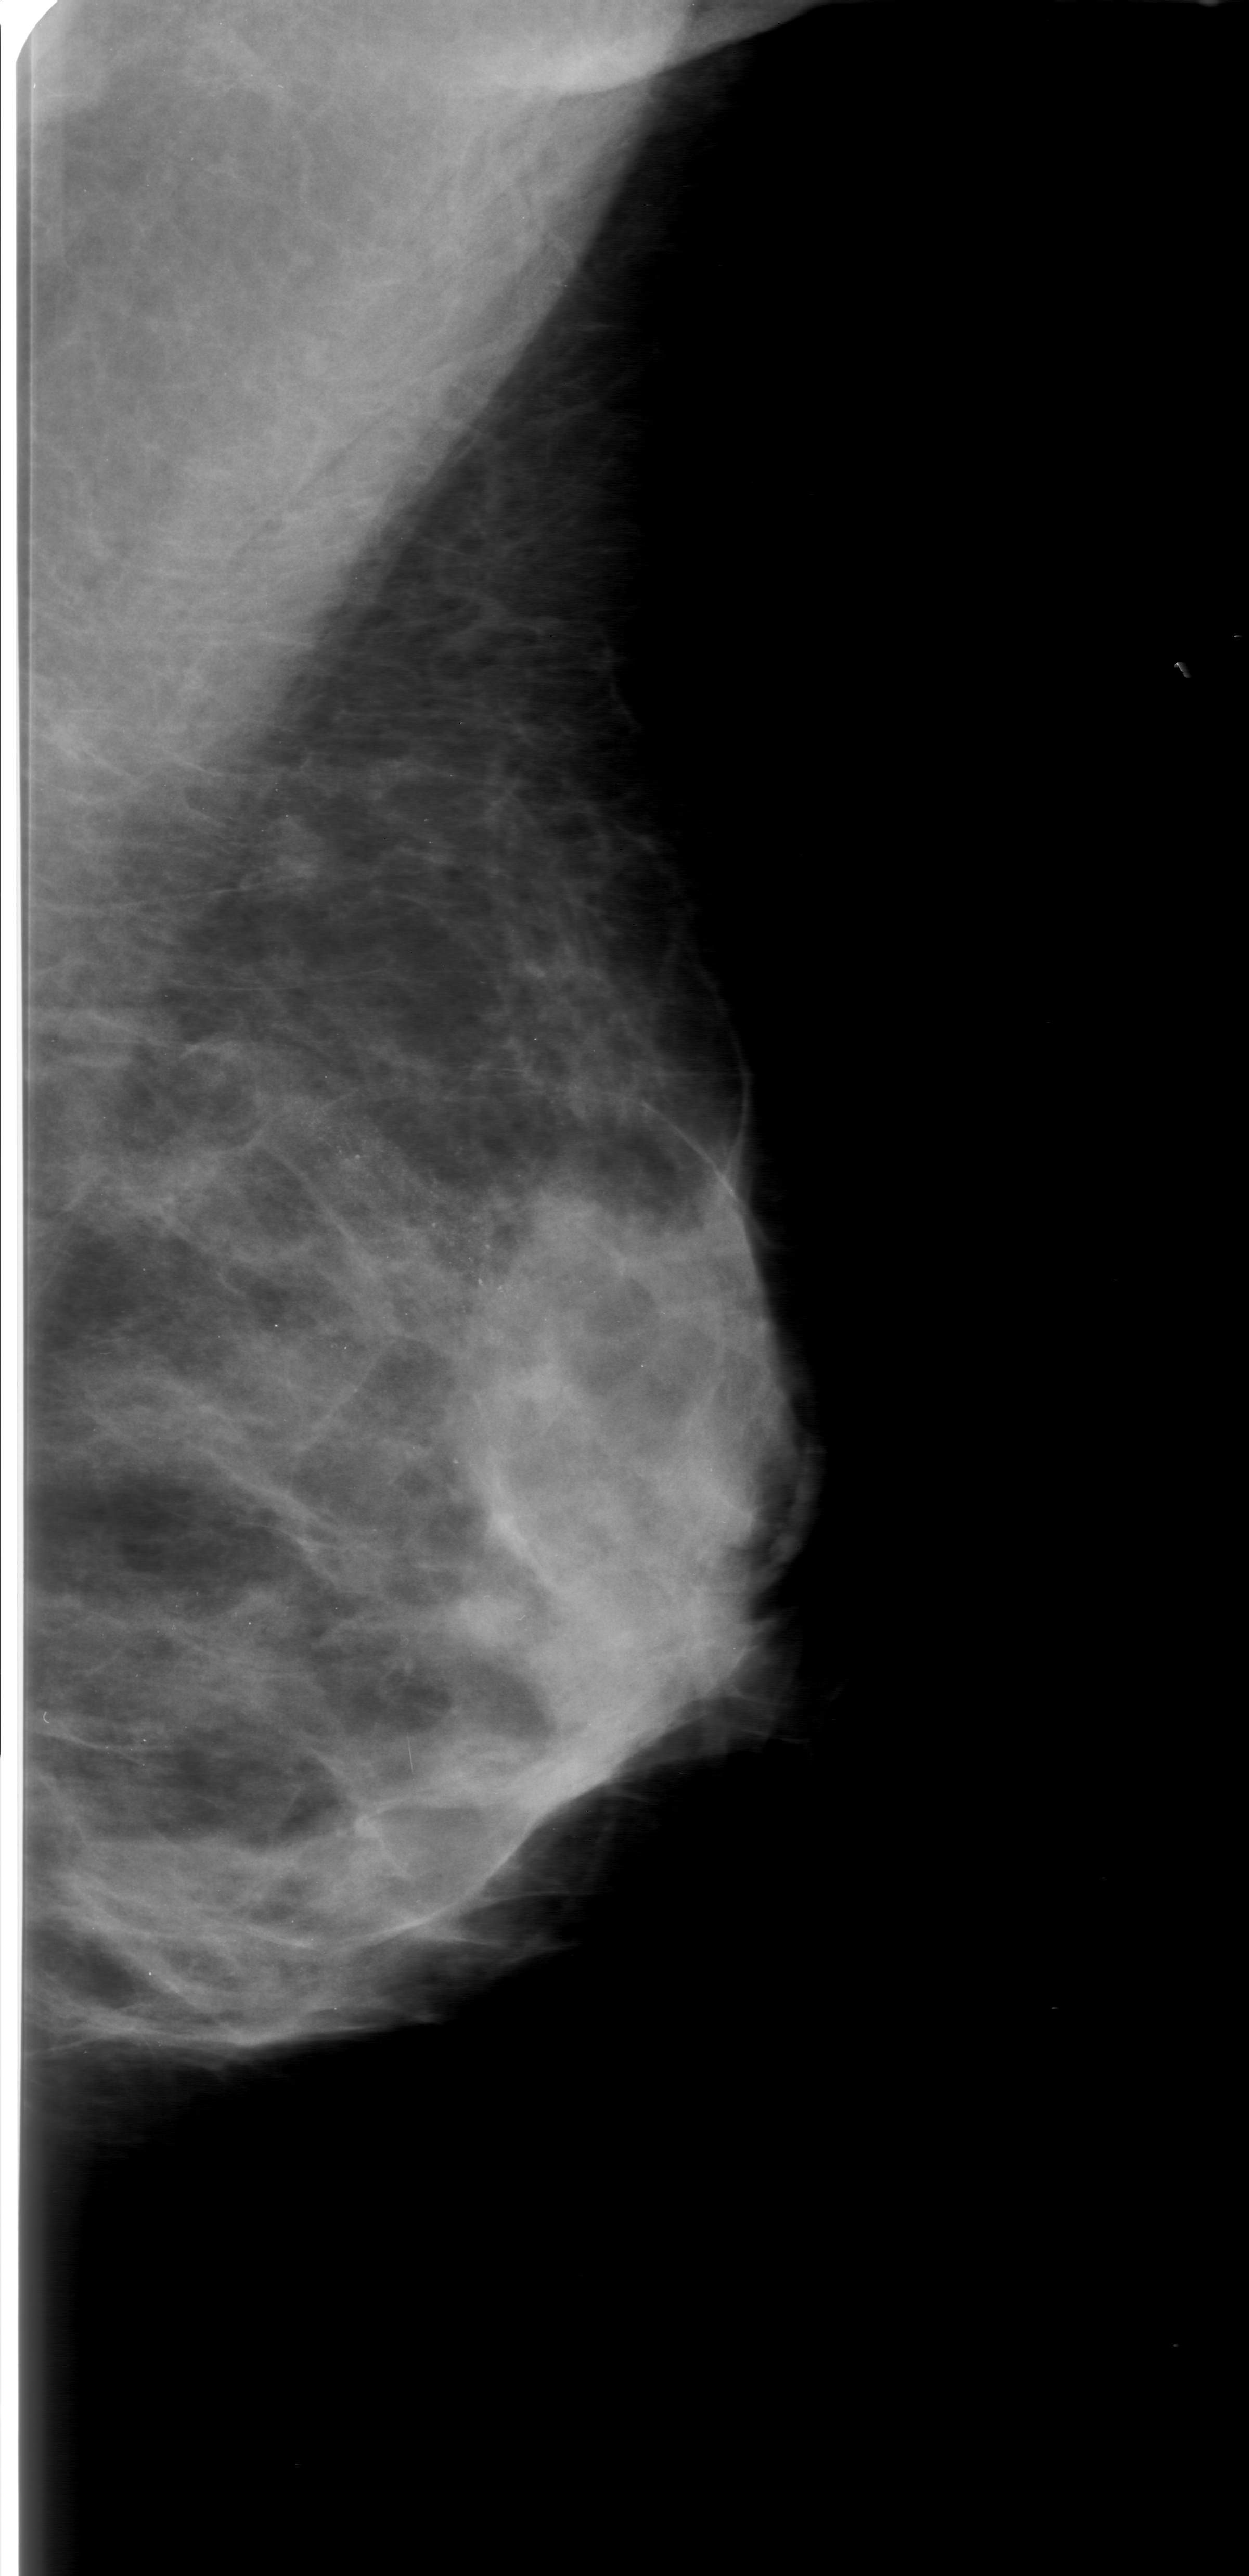
Mammogram (digitized film); left breast; mediolateral oblique (MLO) view; BI-RADS breast density category 3 (scale 1–4); 1249 × 2576 image matrix.
Expert-marked regions of interest on this image (one box per marked abnormality):
- calcifications, morphology amorphous, distribution segmental; BI-RADS assessment category 0 (incomplete: needs additional imaging); pathology (as recorded): benign: box from (x=161, y=991) to (x=703, y=1436) px